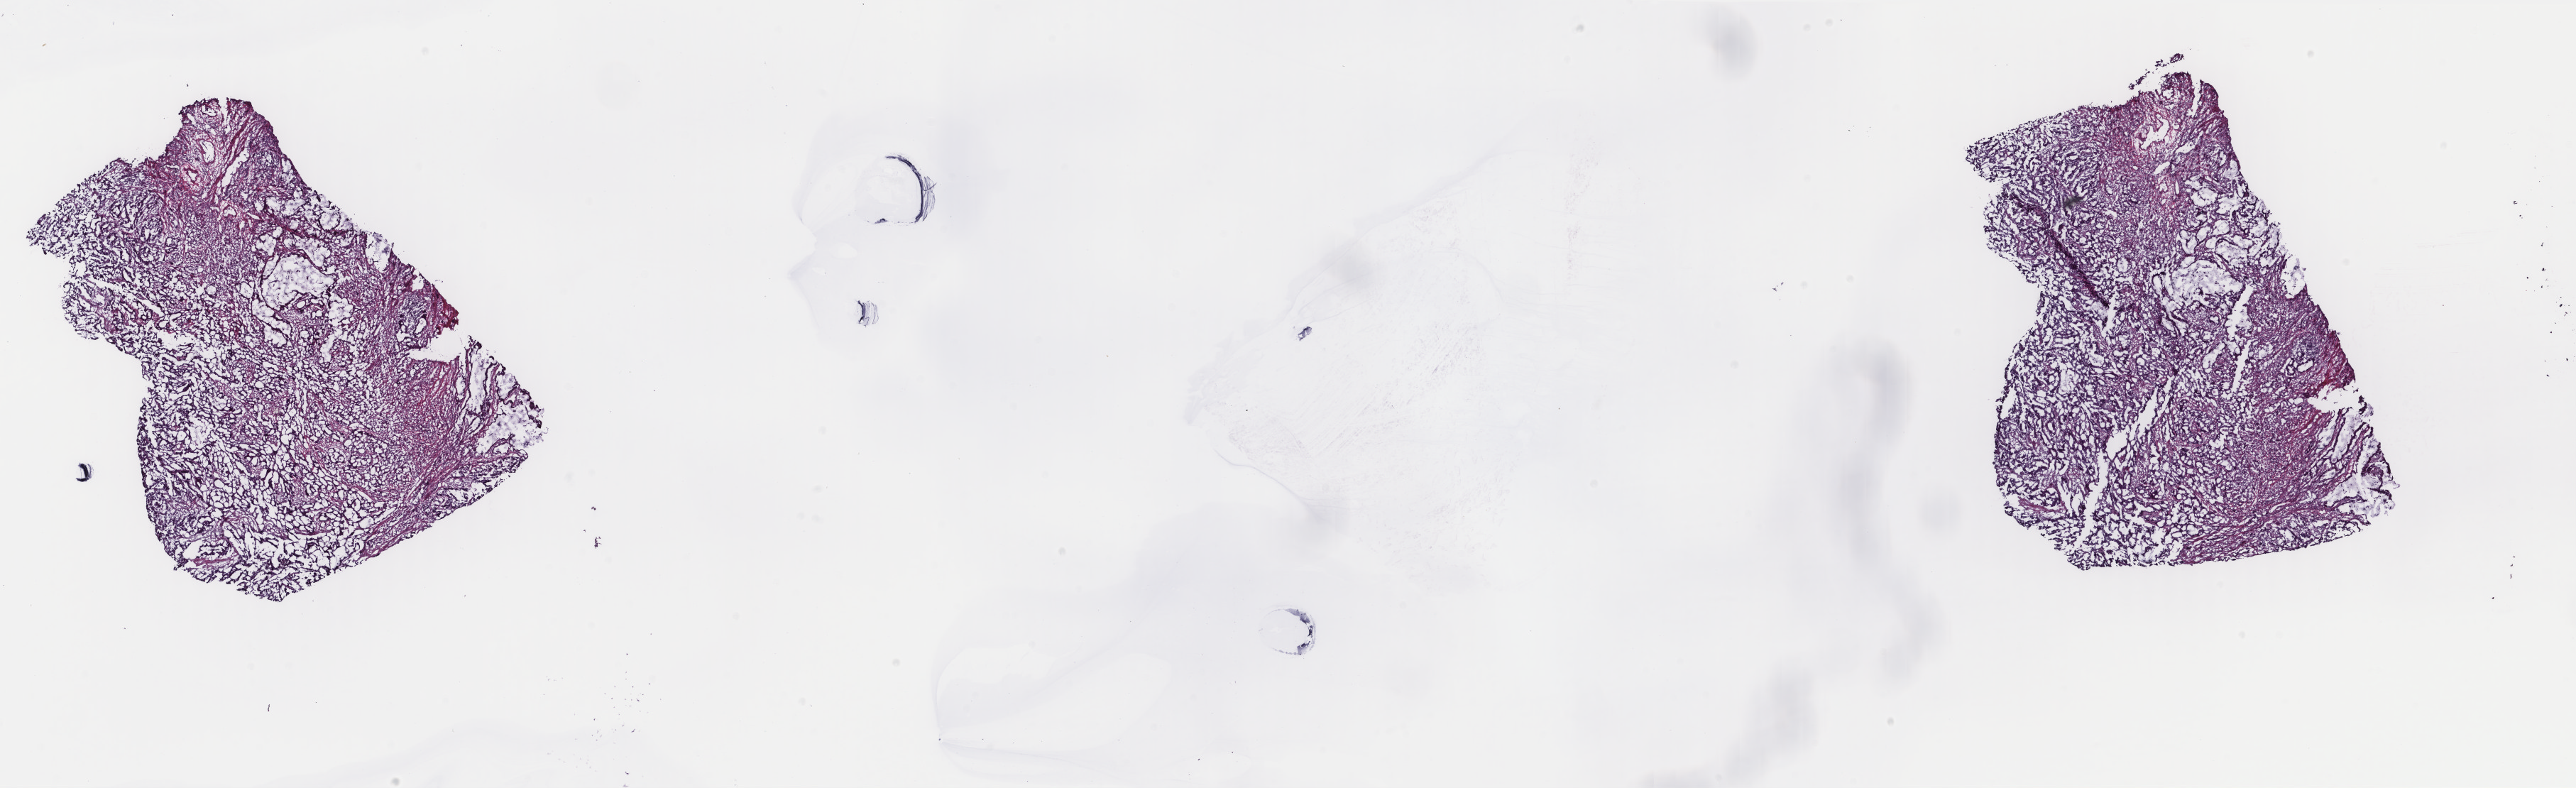
Digitized H&E-stained tissue section (whole slide), low-resolution overview of the scanned area, about 28.8 x 8.8 mm. Frozen section from the top of the tissue portion. Primary tumour sample from the colon. Patient: female, age at initial diagnosis 67 years. Pathologist review of this section (percent, as recorded): tumour cells 100%, tumour nuclei 75%, normal cells 0%, stromal cells 0%, necrosis 0%. Inflammatory infiltration, as recorded: lymphocyte infiltration 0%, monocyte infiltration 0%, neutrophil infiltration 0%.
AJCC pathologic stage: IIA. TNM: T3 N0 M0. Pathologic diagnosis: Adenocarcinoma, NOS (cecum). Lymph nodes positive (case pathology): 0 of 28 examined.